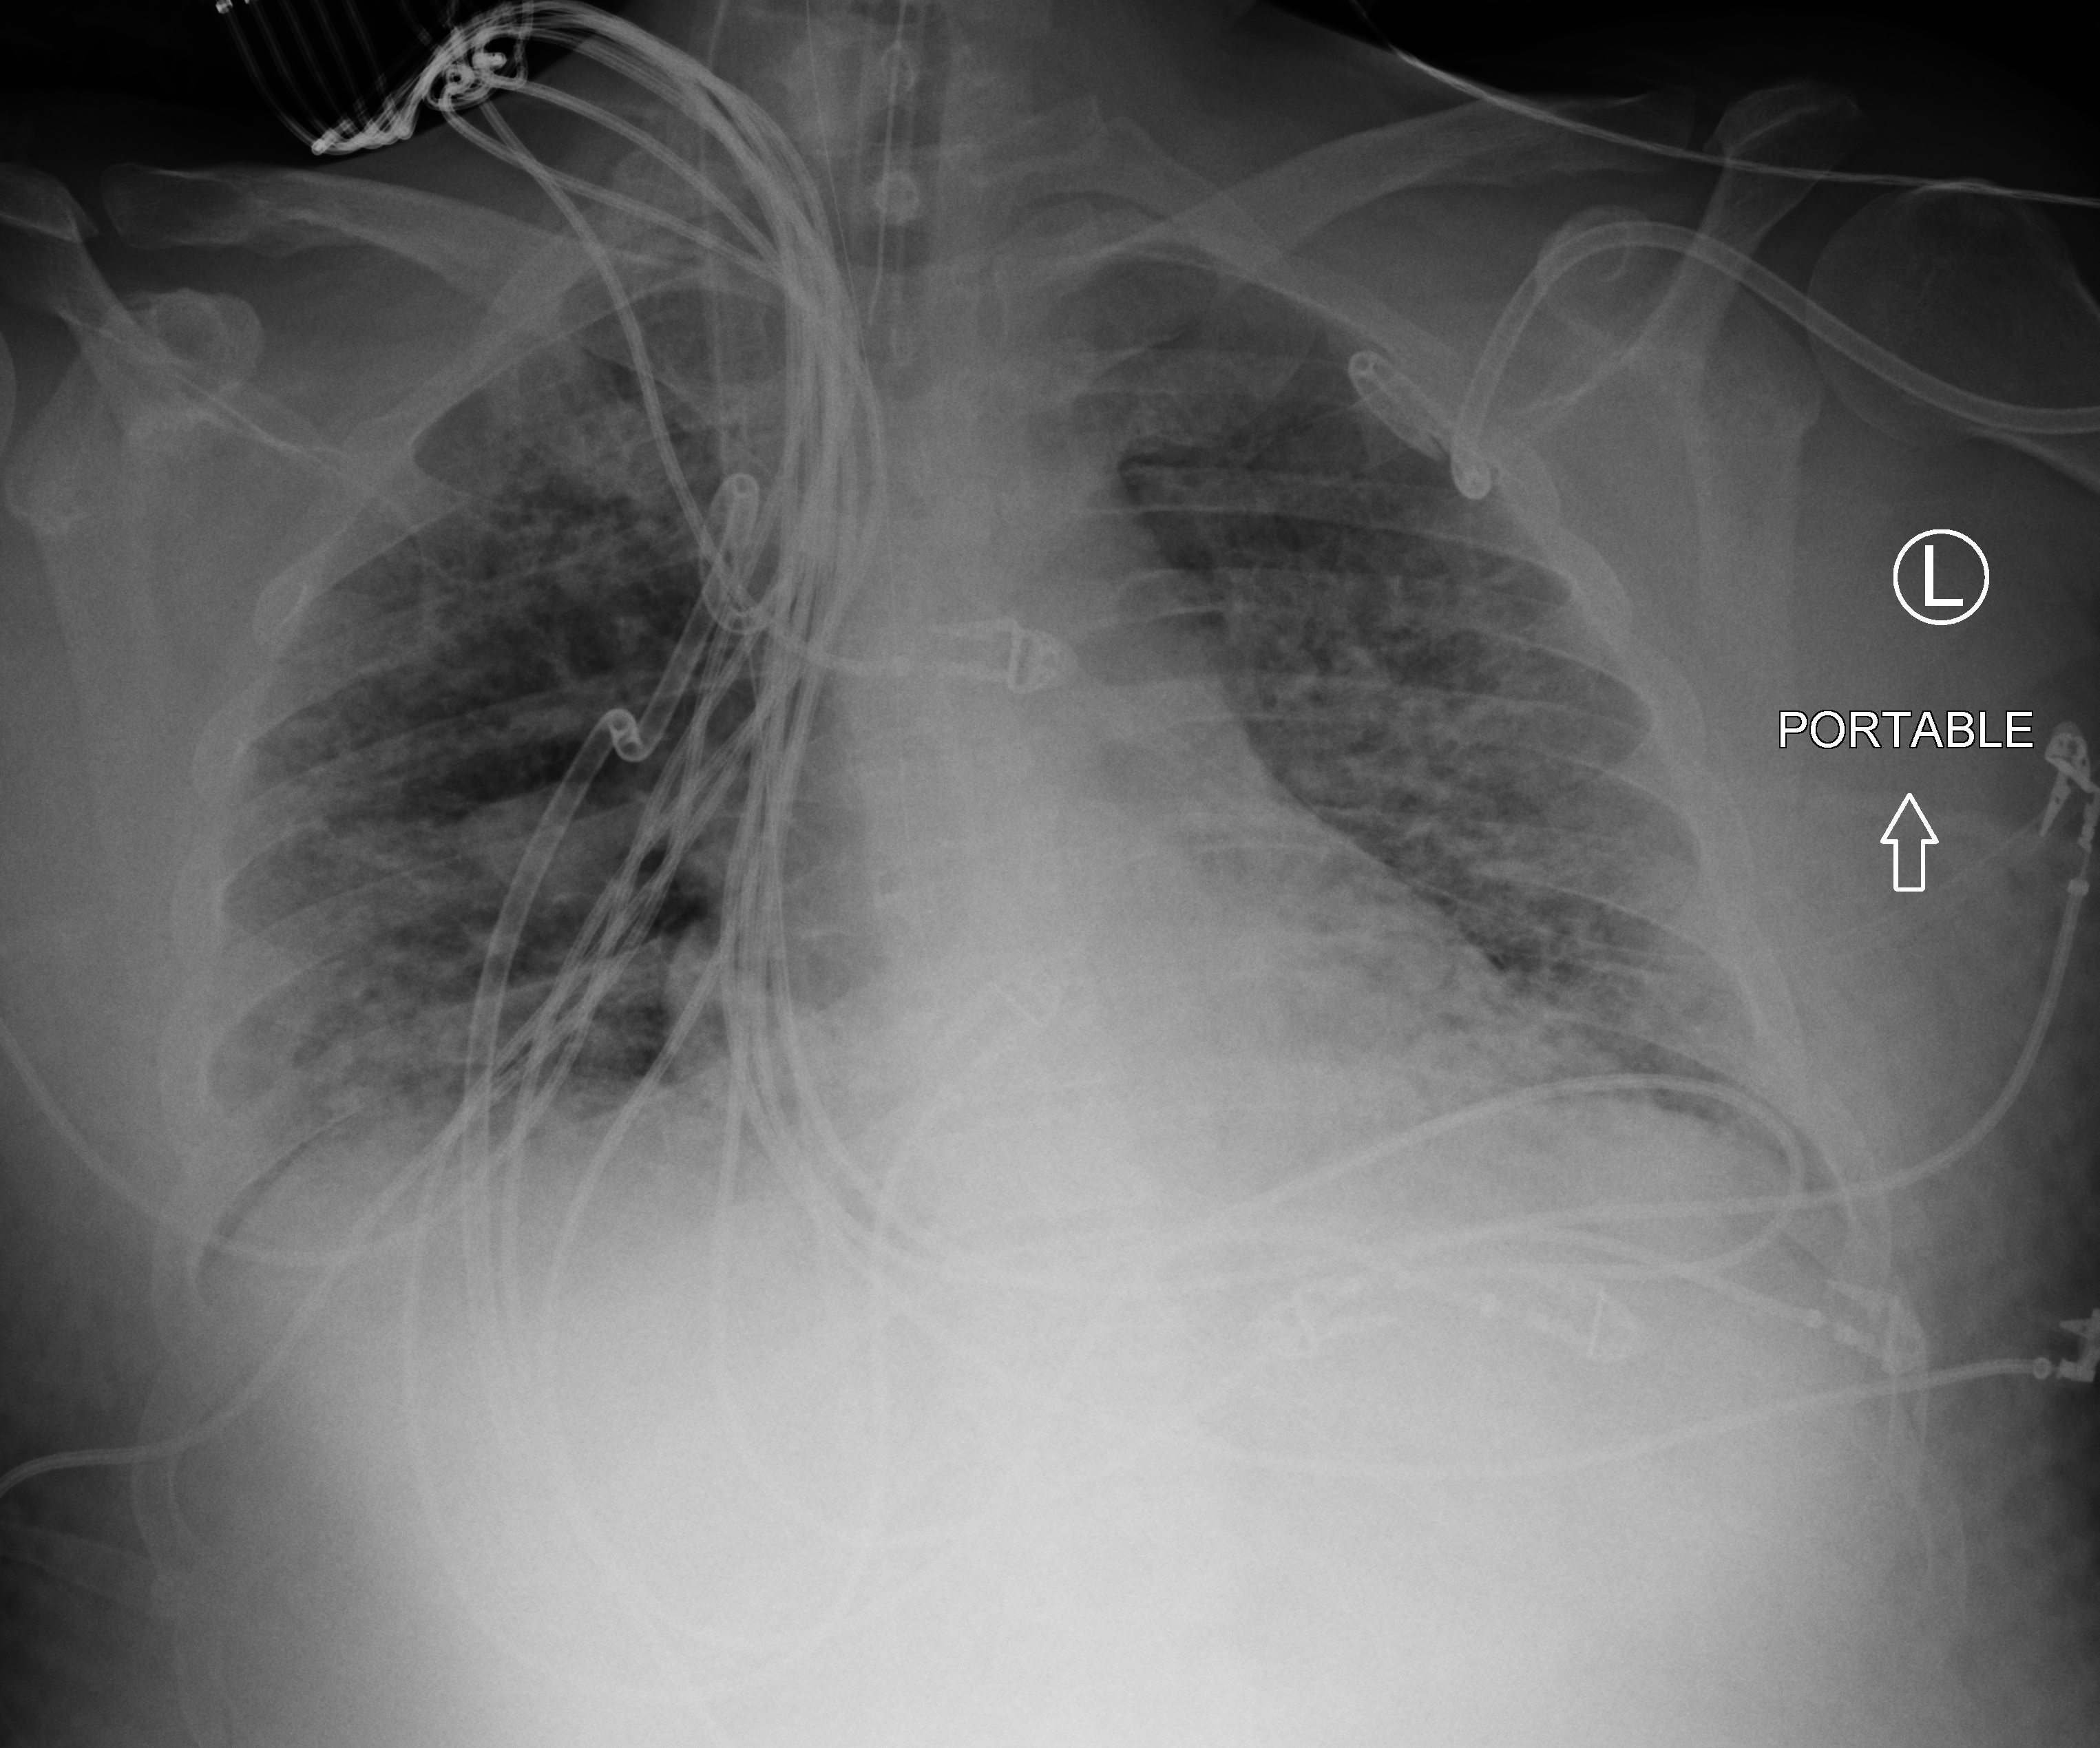
Bedside chest radiograph (computed radiography); anteroposterior (AP) projection. Patient hospitalised with COVID-19, aged 18–59 years.
Hospital-stay facts (about this admission, not read from this image; timing relative to this image not recorded):
- admitted to intensive care during this hospital stay: yes